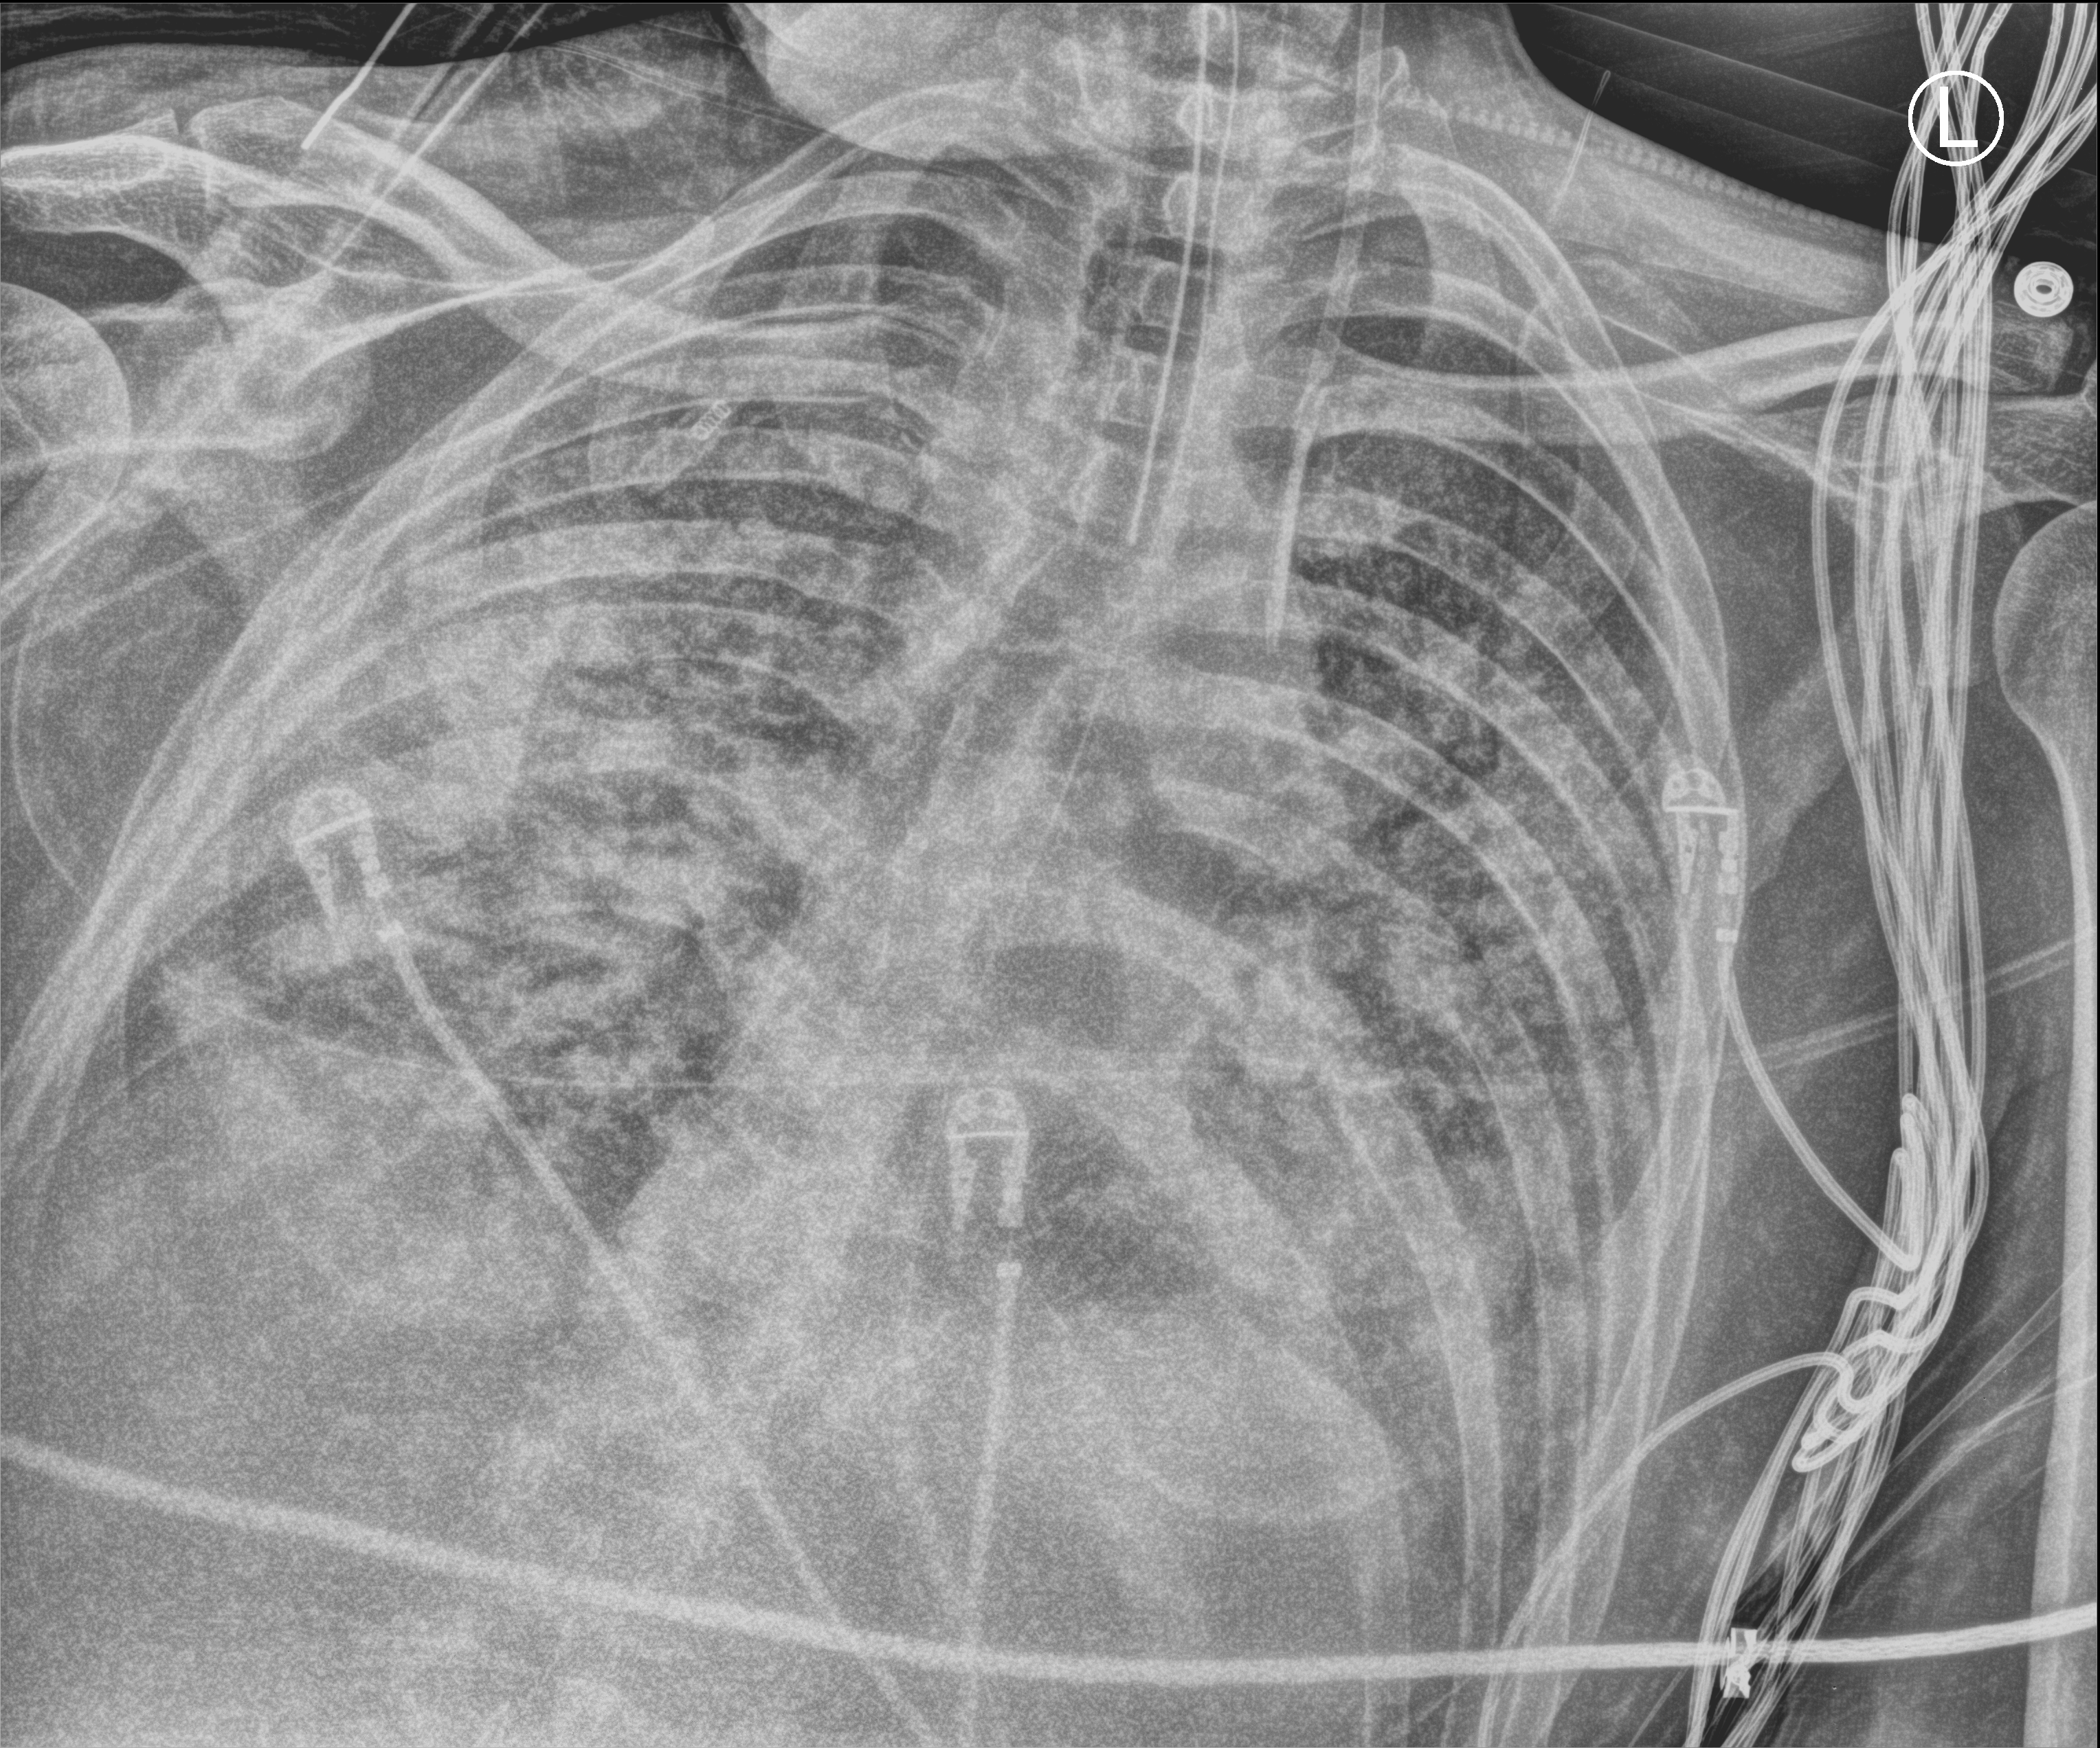
Chest X-ray (portable); anteroposterior (AP) projection. Patient hospitalised with COVID-19; male, aged 18–59 years.
Admission-level facts for this patient (not findings on this image; timing relative to this image not recorded): length of hospital stay: 75 days.